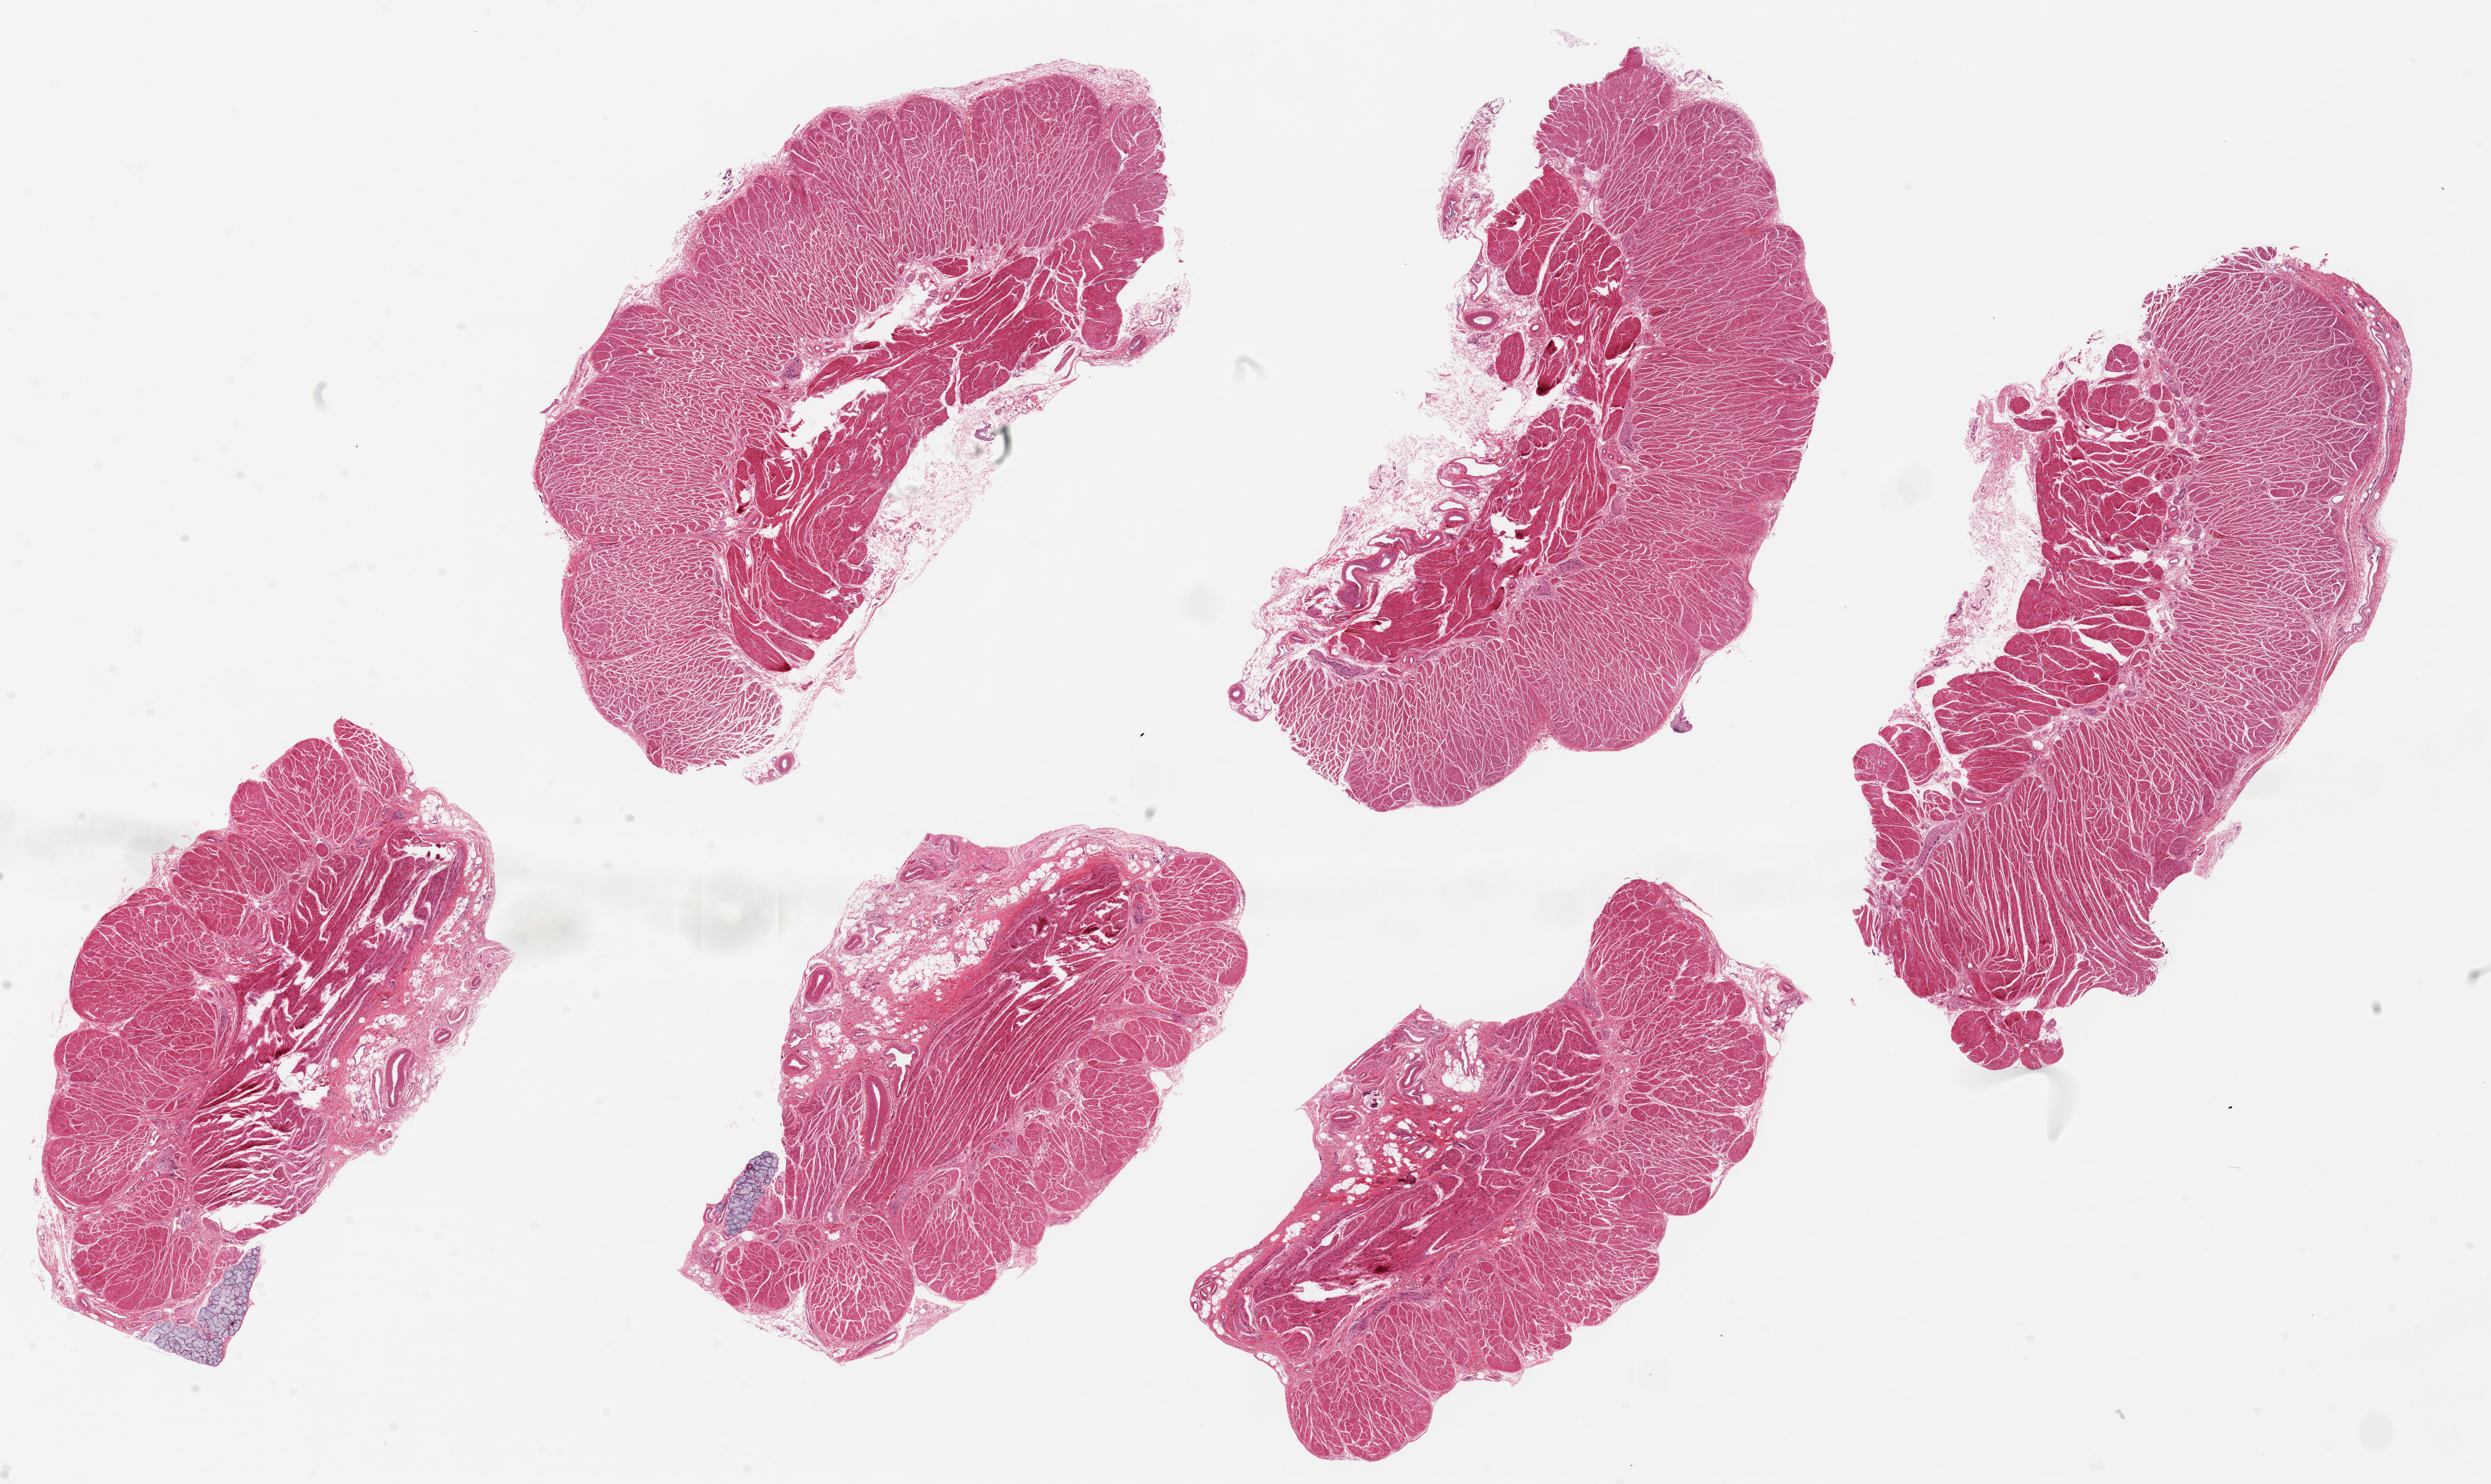
Digitized hematoxylin and eosin (H&E)-stained section, low-resolution overview of the scanned area, about 31.5 x 18.8 mm, PAXgene-fixed, paraffin-embedded tissue, section of gastroesophageal junction (target tissue), tissue donor sample. Donor: male.
Pathologist's review note for this sample: 6 pieces, ~8x4mm, all muscularis, excellent specimens.